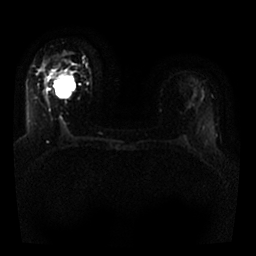
Breast MRI, one axial slice. Position 15 of 25 along the scan axis. Diffusion-weighted series; image 2 of 4 stored at this slice position (different b-values; order by instance number). 1.5 T. 4 mm slice thickness. 256 × 256 image matrix, field of view 330 × 330 mm. Female patient.
Annotated regions visible in this slice (manually delineated by an expert):
- tumour on diffusion-weighted imaging: bounding box <54,73,70,81> (left, top, right, bottom; pixels)